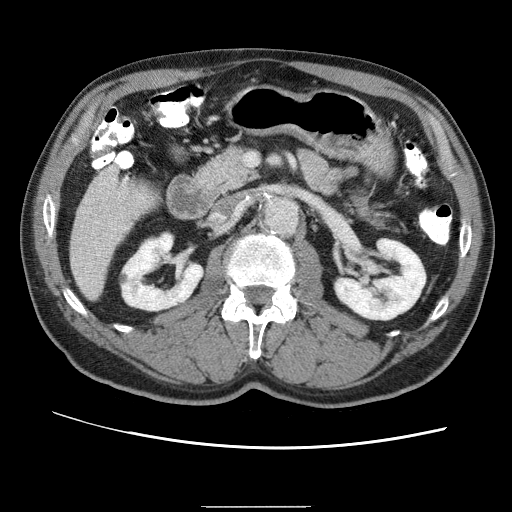
Contrast-enhanced abdominal CT (liver protocol), one axial slice. Position 12 of 75 along the scan axis. Reconstruction kernel STANDARD. 120 kVp. One of 2 acquisitions stored at this slice position. Soft-tissue window (W 400 / L 40 HU). 2.5 mm slice thickness. 512 × 512 image matrix, field of view 360 × 360 mm. From the clinical record (not read from this slice): diagnosis: hepatocellular carcinoma (patient treated with transarterial chemoembolisation; whether this scan precedes or follows treatment is not stated here); TNM stage (as recorded): Stage-II; Child-Pugh class: A.
Annotated regions visible in this slice (semi-automatically segmented with operator editing):
- liver parenchyma outside the tumour (the mass and vessels are separate outlines, so this box may not span the whole liver): bounding box <70,168,122,291> (left, top, right, bottom; pixels)
- liver vessels: <76,170,115,259>